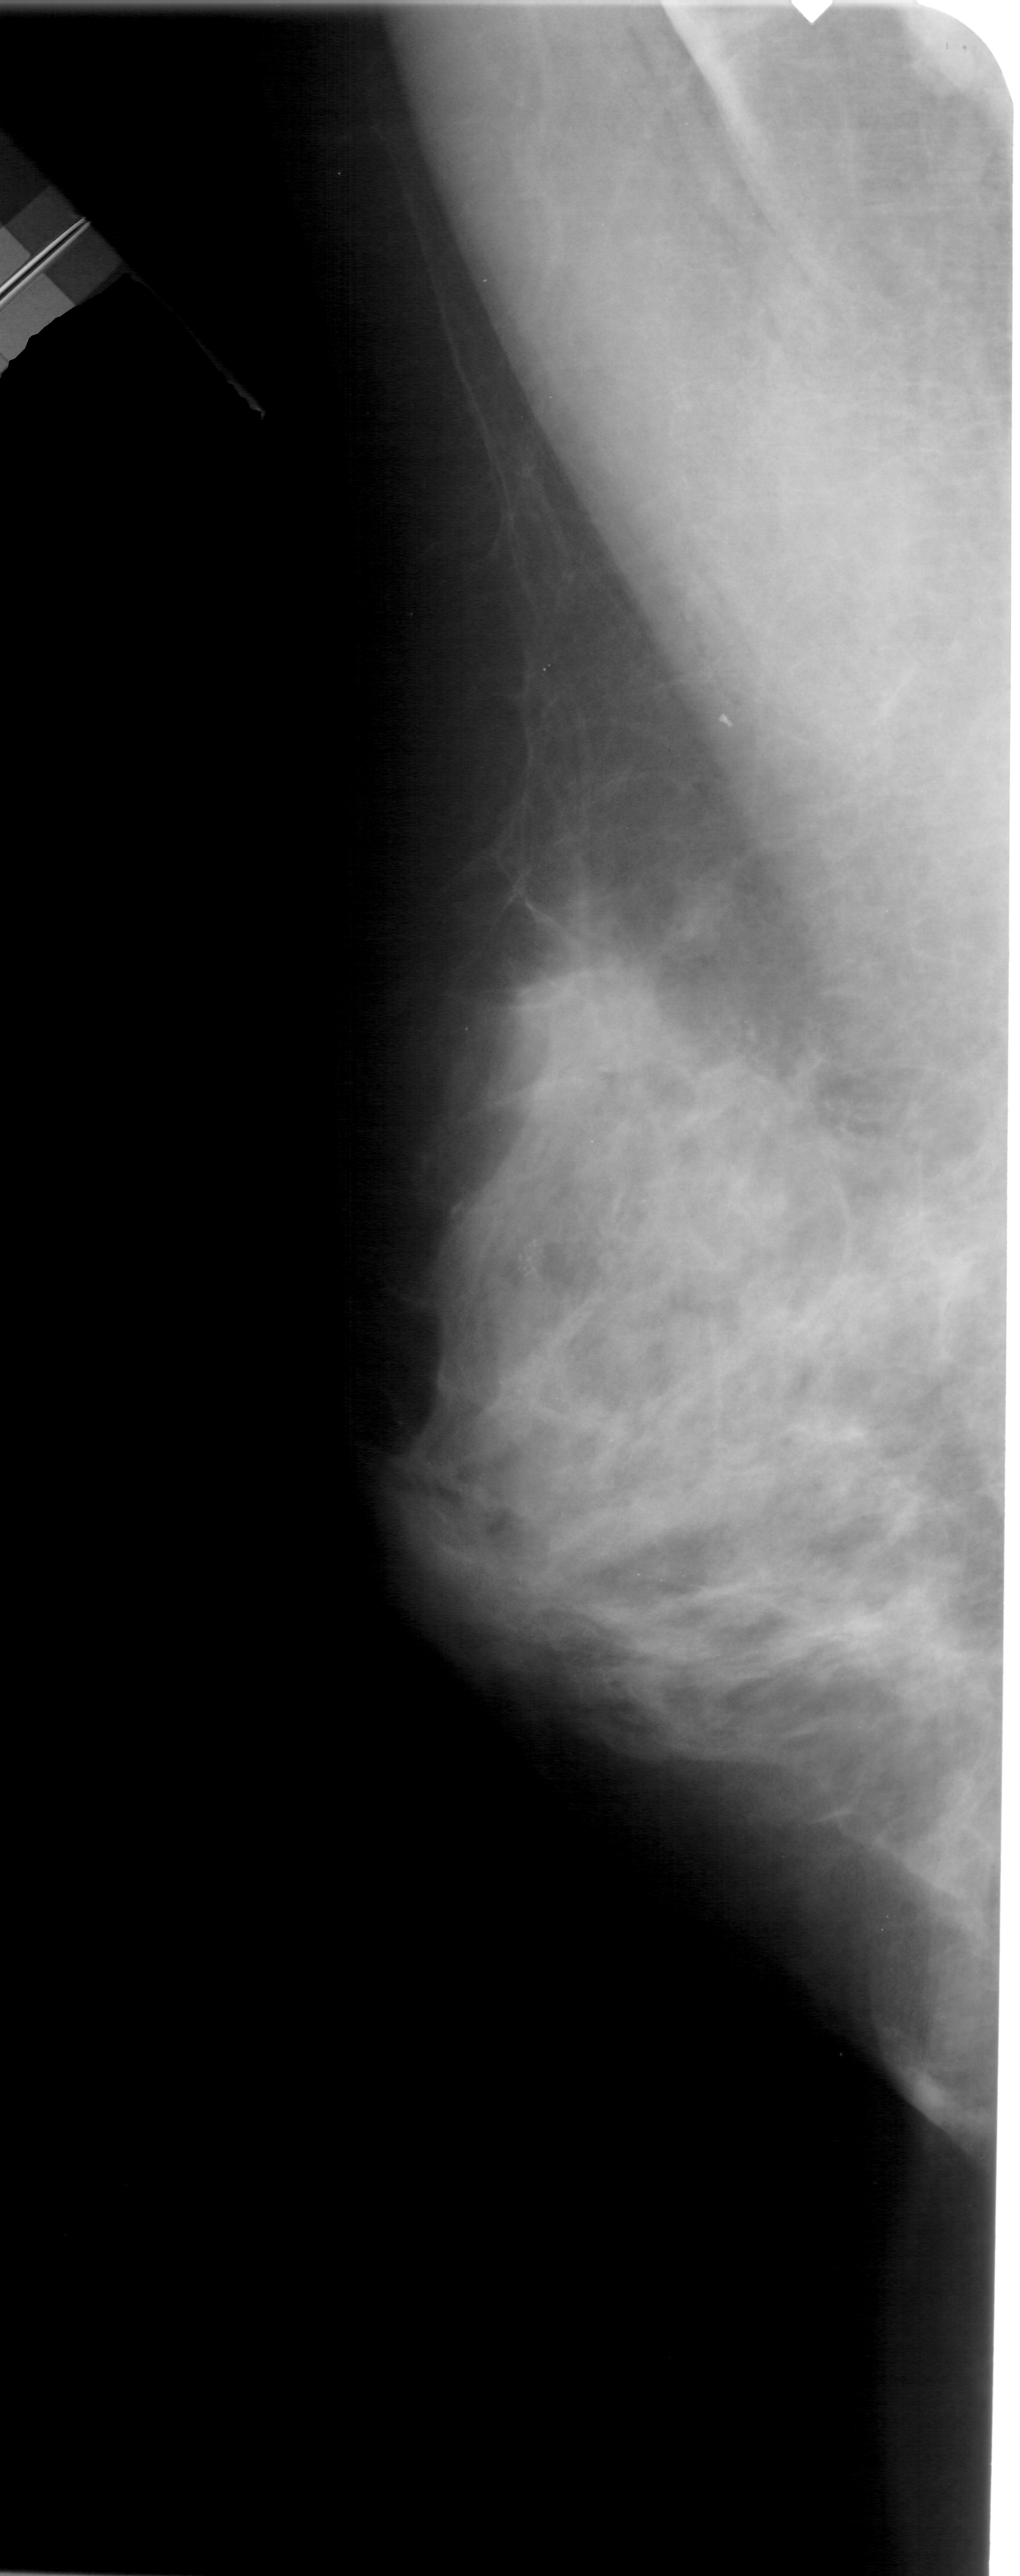
Digitized screen-film mammogram; left breast; MLO view; BI-RADS breast density category 4 (scale 1–4).
- Marked abnormality: calcifications, morphology pleomorphic, distribution clustered; BI-RADS assessment category 4; subtlety rating 2 on a 1 (subtle) to 5 (obvious) scale; pathology (as recorded): benign.